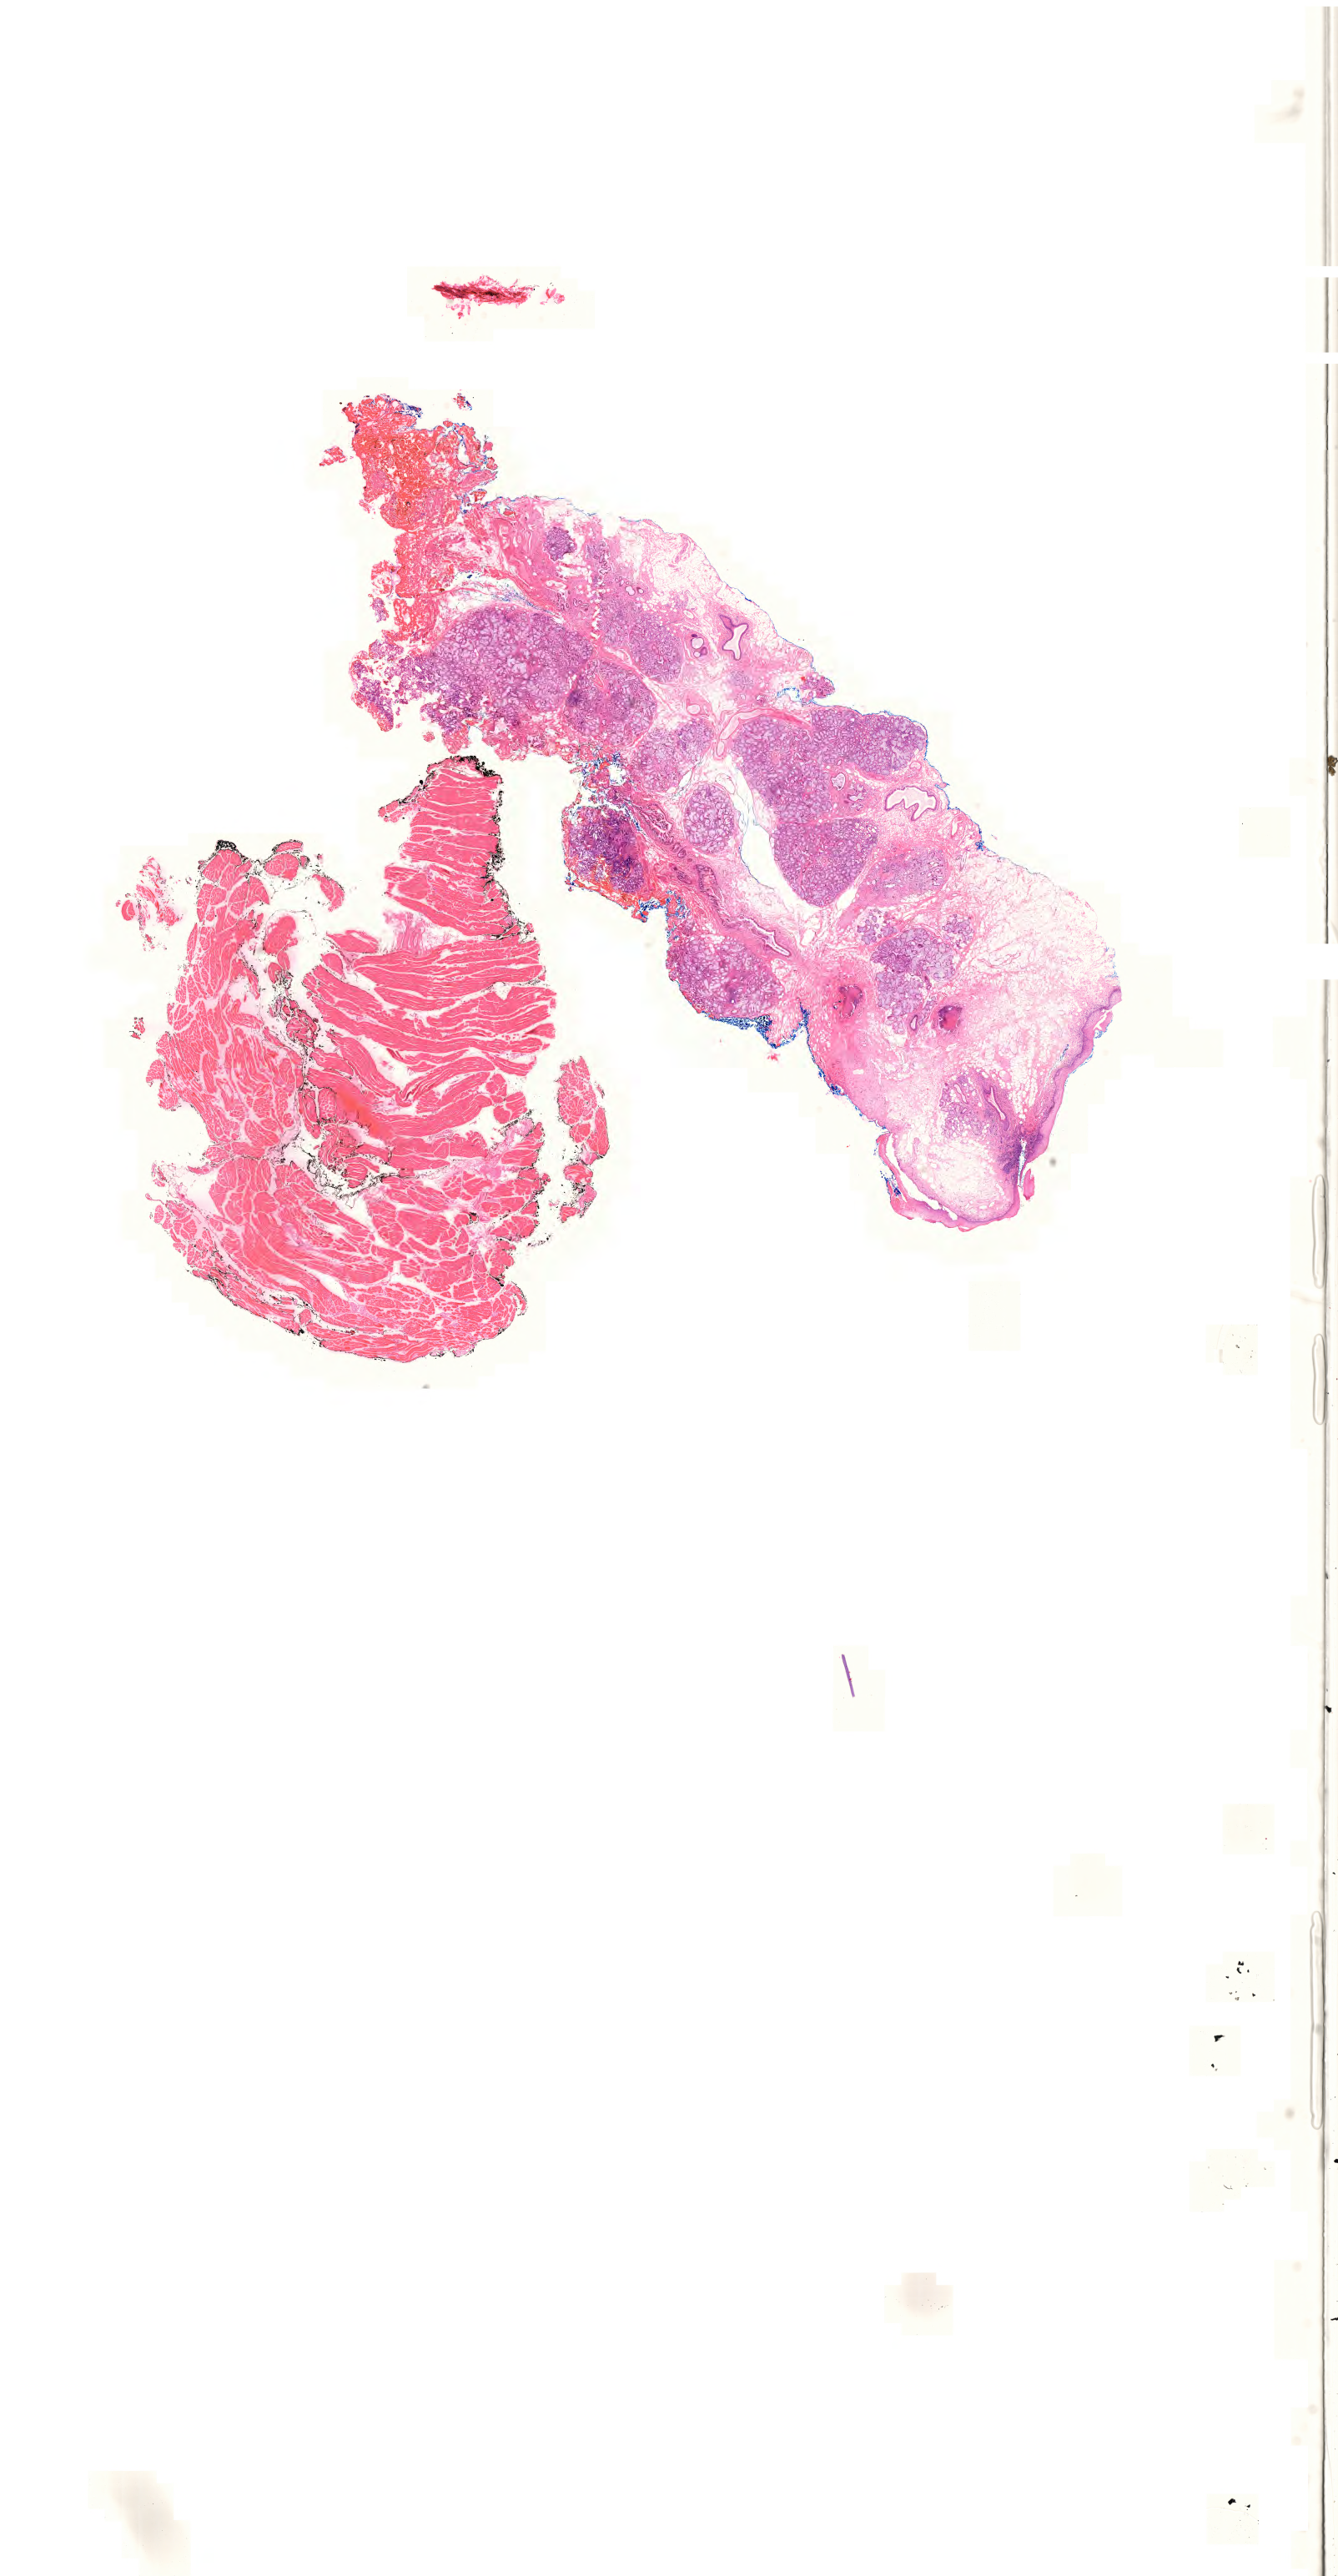
Digitized Hematoxylin and eosin (H&E) stained tissue section (whole slide) — shown as a low-resolution overview of the whole scanned area (about 23.9 x 45.9 mm). Formalin-fixed paraffin-embedded (FFPE) diagnostic section. Sample: primary tumour, head and neck. Male, age 79 years at initial diagnosis. Histologic grade: G3 (poorly differentiated).
Pathologic diagnosis: Squamous cell carcinoma, NOS (floor of mouth, NOS). AJCC pathologic stage: IVA.